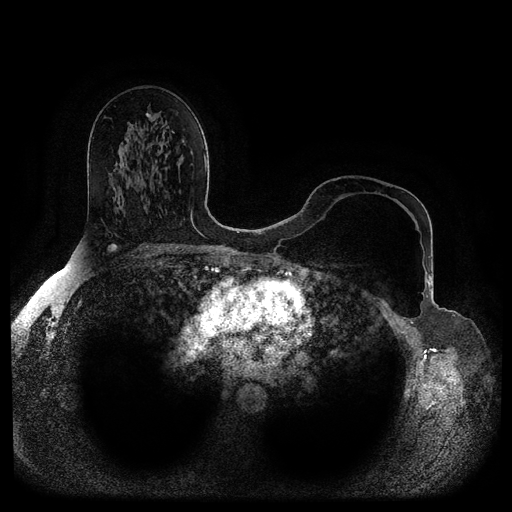
Breast MRI (dynamic contrast-enhanced, multi-phase), one axial slice; position 55 of 116 along the scan axis; dynamic contrast-enhanced series, time point 2 of 5 at this slice position (early post-contrast); 1.5 T; TE 2.6 ms, TR 5.2 ms; 2 mm slice thickness; 512 × 512 image matrix, field of view 380 × 380 mm. Female patient, age 56 years.
Structures marked on this image (semi-automatically segmented with operator editing):
- breast lesion (labelled benign in the annotation): bounding box <146,113,150,117> (left, top, right, bottom; pixels)